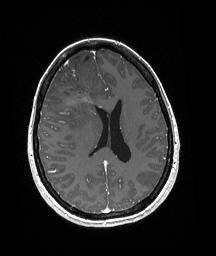
Brain MRI from a brain-tumour surgery series, one axial slice. Position 81 of 192 along the scan axis. T1-weighted post-contrast. 1 mm slice thickness. 216 × 256 image matrix. From the clinical record (not read from this slice): histopathology: Oligodendroglioma; WHO grade: 3; IDH mutation: yes; tumour location: Right Frontal.
Structures marked on this image (manually delineated by an expert):
- tumour: bounding box <56,81,96,103> (left, top, right, bottom; pixels)